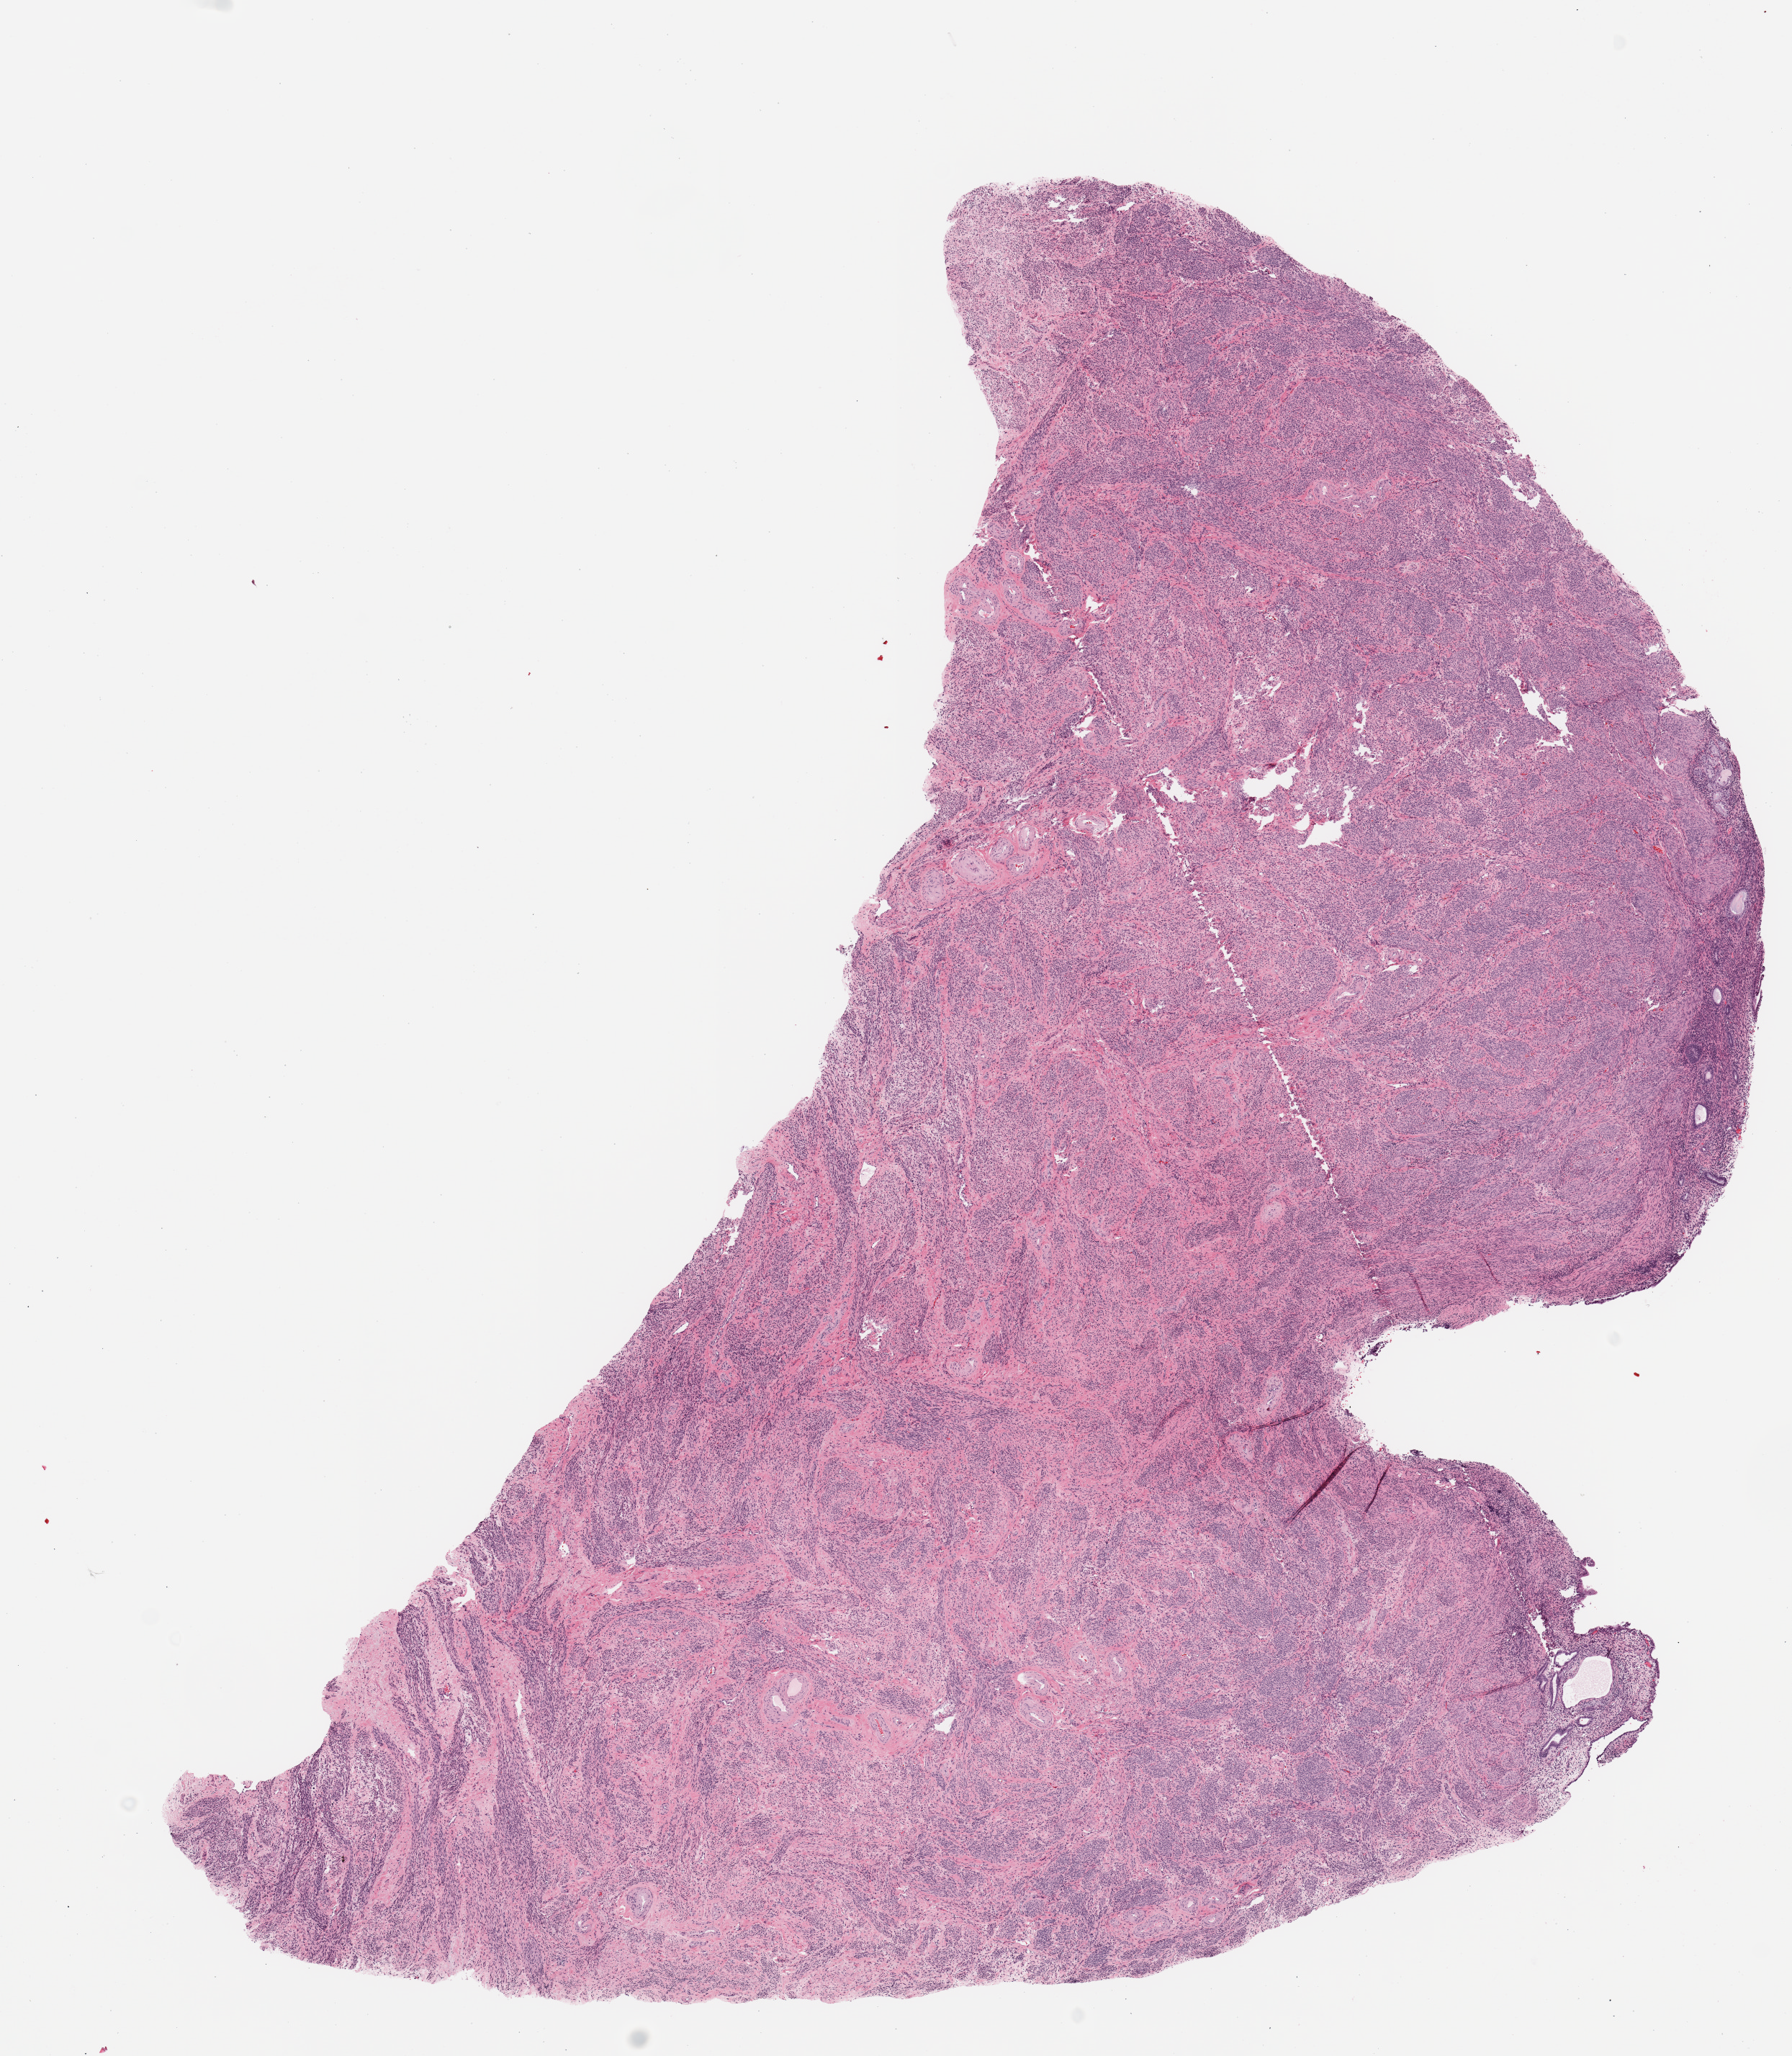
Whole-slide histology image, H&E, whole scanned area (about 9.8 x 11.3 mm) shown as a low-resolution overview, normal (non-tumour) tissue sample, sampled site: uterus. Female, 64 y/o.
This section: normal (non-tumour) tissue from the same patient. Patient diagnosis: Endometrioid adenocarcinoma, NOS.